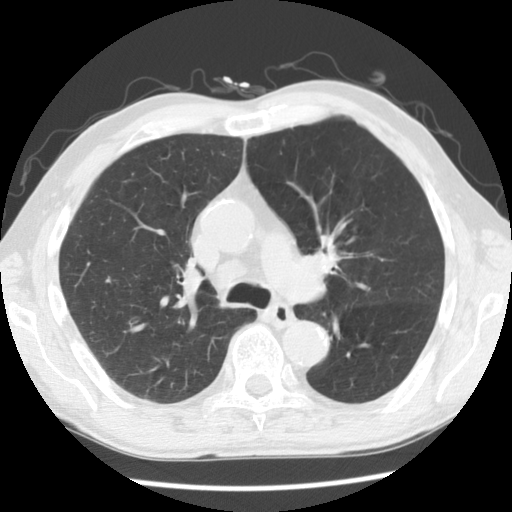
Chest CT (low-dose screening protocol), one axial image, first (baseline) screen, lung window (W 1500 / L -600 HU), 140 kVp. Male, age 68 years at enrolment. Current smoker at enrolment.
Lesion marked by an expert reader, bounding box (x1, y1, x2, y2) in pixels: (300, 223, 355, 280). Screening reader's record for this exam: no non-calcified nodule ≥4 mm recorded. Official screen result: negative screen, minor abnormalities not suspicious for lung cancer. Lung cancer was diagnosed 215 days after this screen: squamous cell carcinoma, NOS, left hilum, stage IIB (AJCC 6th edition), 32 mm at pathology.